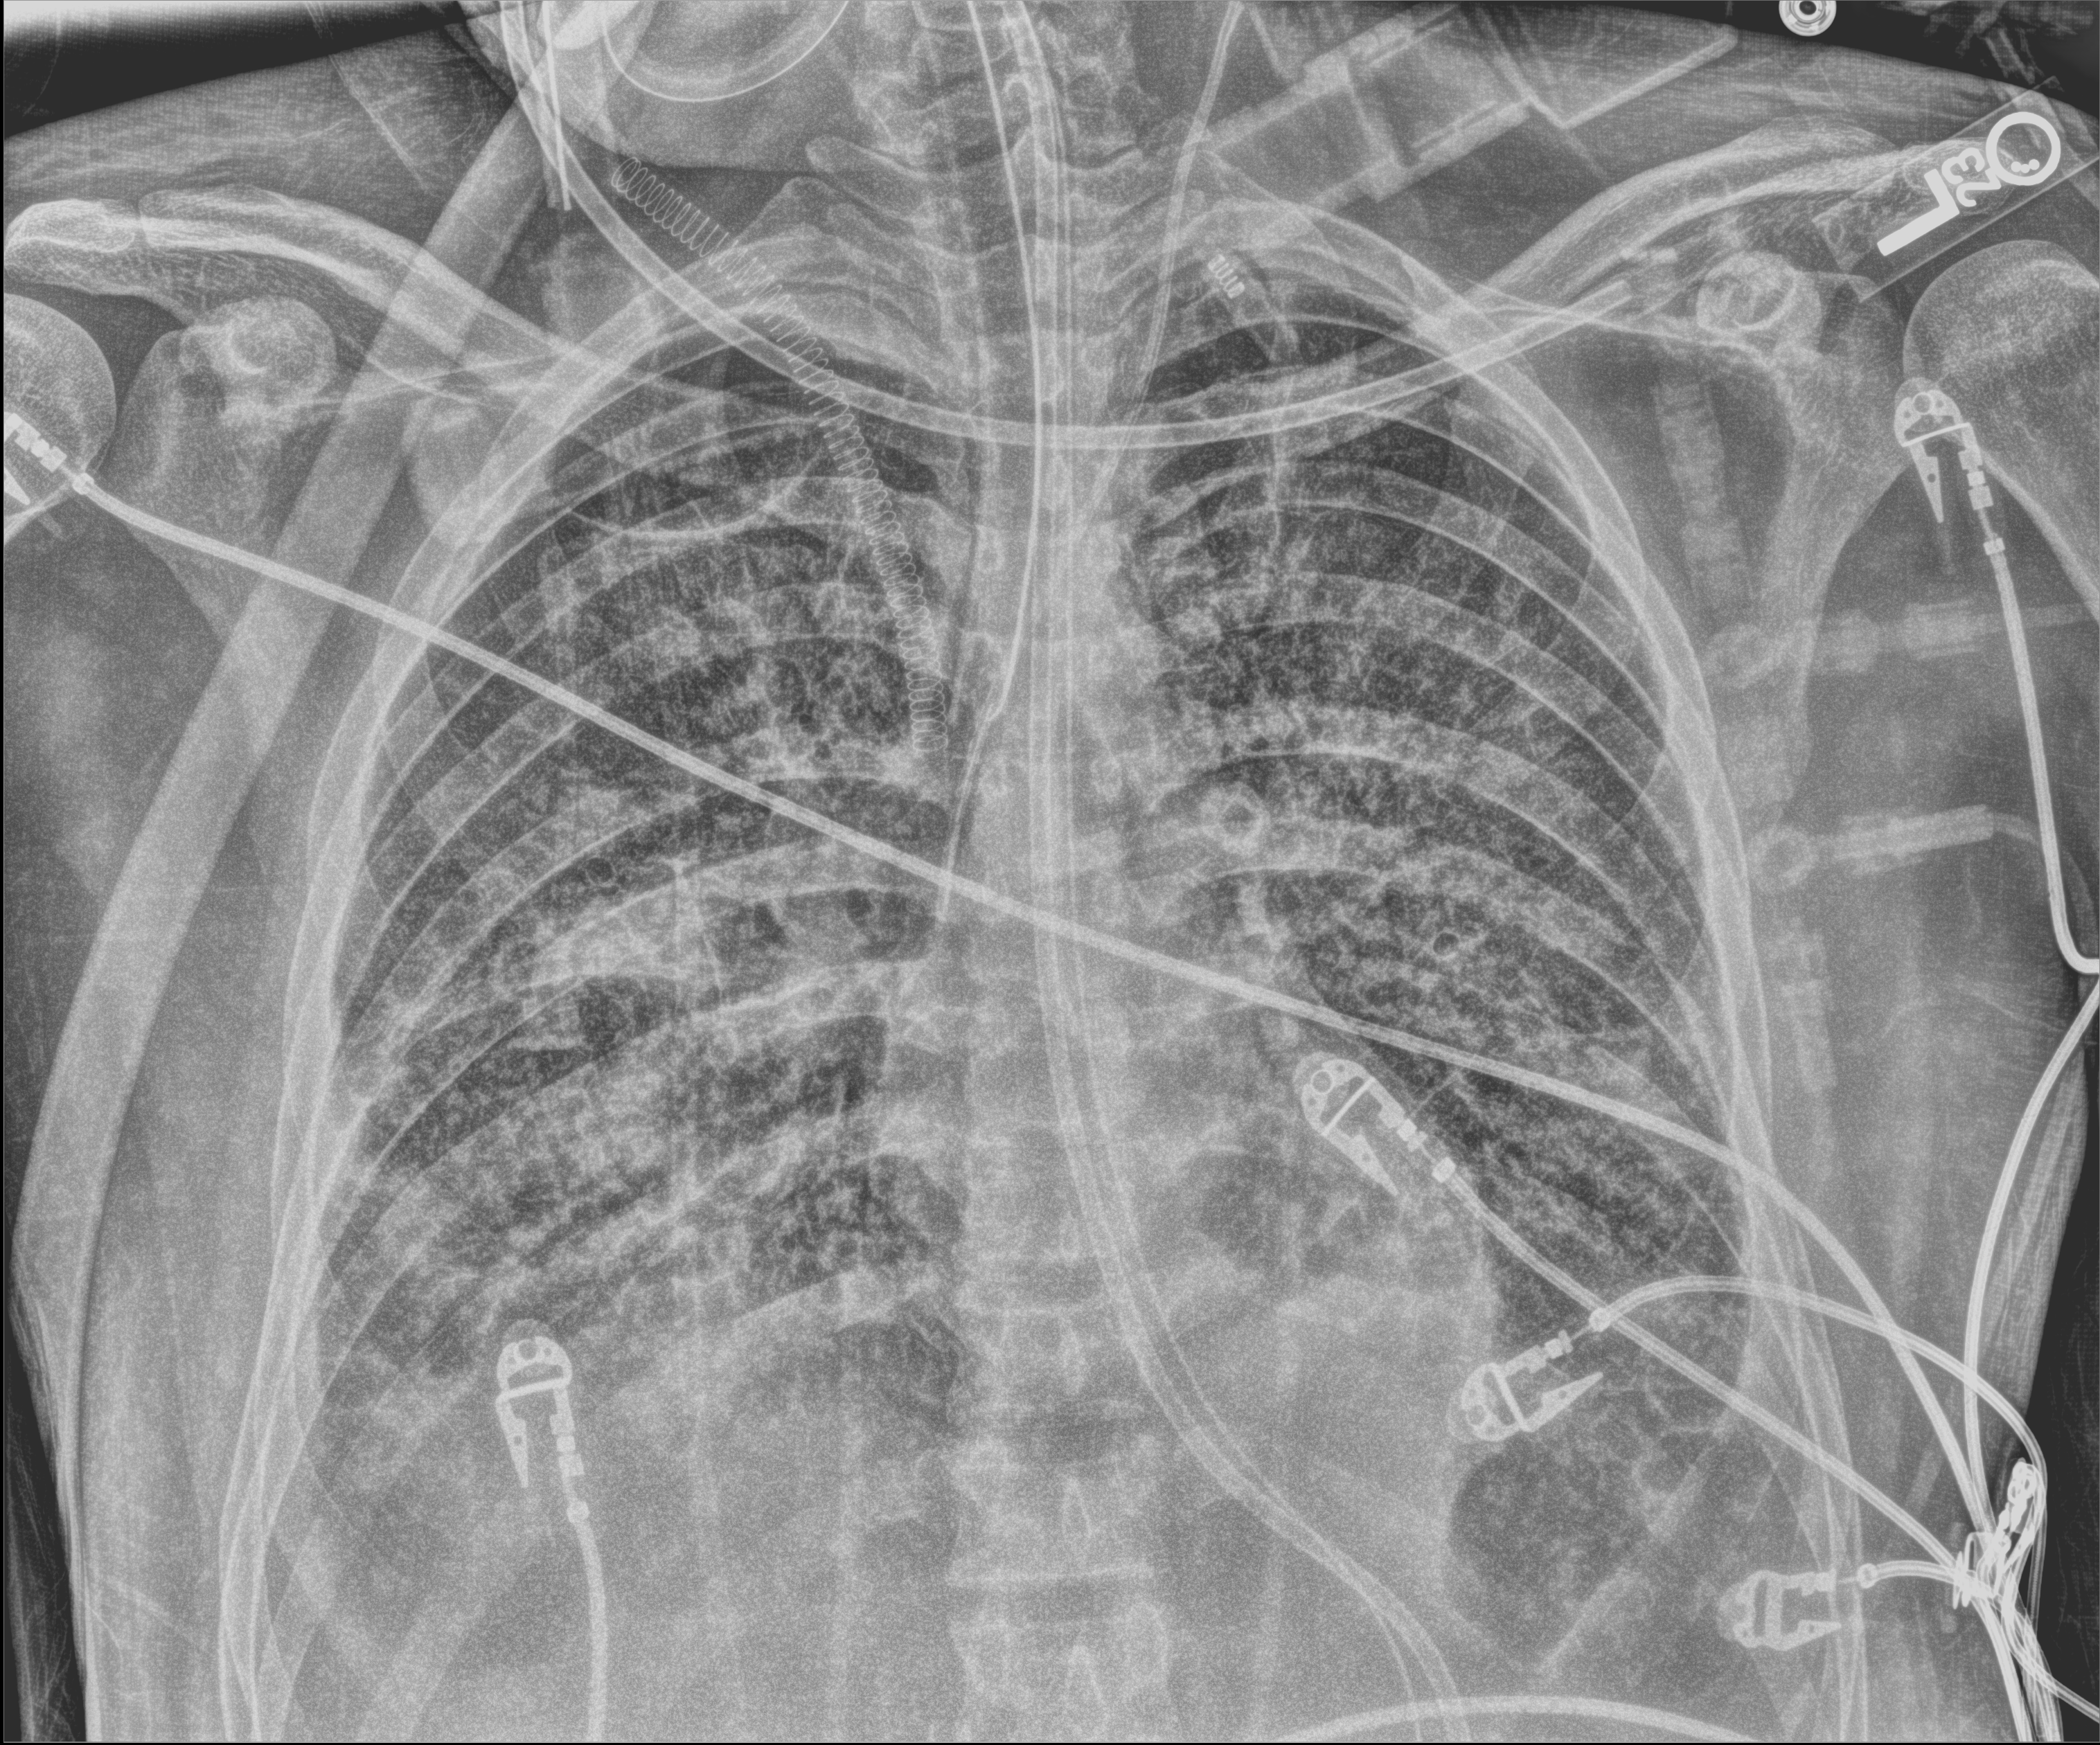
Bedside chest radiograph (digital radiography); anteroposterior (AP) projection. Adult patient hospitalised with COVID-19, age 18–59 years.
Admission-level facts for this patient (not findings on this image; timing relative to this image not recorded): mechanically ventilated during this hospital stay: yes; admitted to intensive care during this hospital stay: yes; chronic kidney disease (admission record): no.